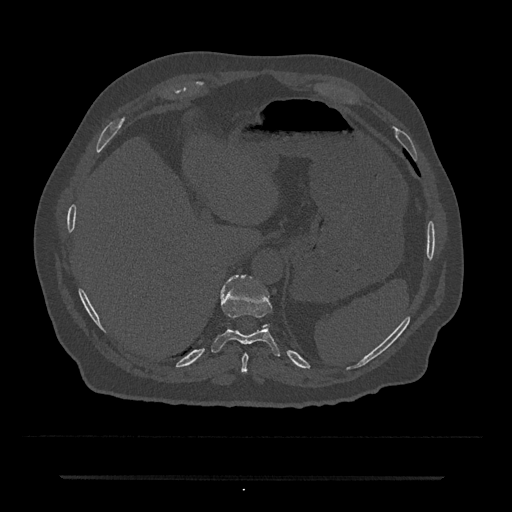
CT including the spine, one axial slice. Slice 228 of 797 in the series (ordered by position). Reconstruction kernel Br40s/3. 120 kVp. Bone window (W 1800 / L 400 HU). 0.5 mm slice thickness. 512 × 512 image matrix, field of view 437 × 437 mm. Patient: male, 69 years. From the clinical record (not read from this slice): primary cancer: prostate.
Structures marked on this image (semi-automatic segmentation, software-assisted and operator-edited):
- T10 vertebra: box from (x=211, y=275) to (x=280, y=356) px
- T11 vertebra: (x=225, y=275)–(x=267, y=327)
- T9 vertebra: (x=242, y=353)–(x=249, y=373)